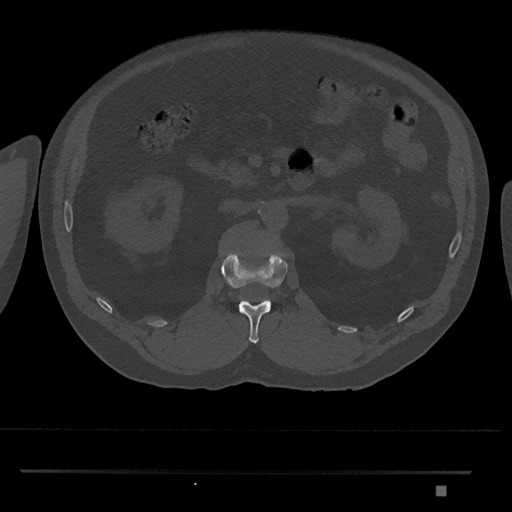
CT including the spine, one axial slice; position 804 of 1134 along the scan axis; reconstruction kernel Br40s/3; bone window (W 1800 / L 400 HU); 0.5 mm slice thickness; 512 × 512 image matrix. Patient: male, 65 years. Case-level facts recorded for this patient, not image findings: primary cancer: prostate.
Structures marked on this image (semi-automatically segmented with operator editing):
- L1 vertebra: box from (x=220, y=250) to (x=288, y=344) px